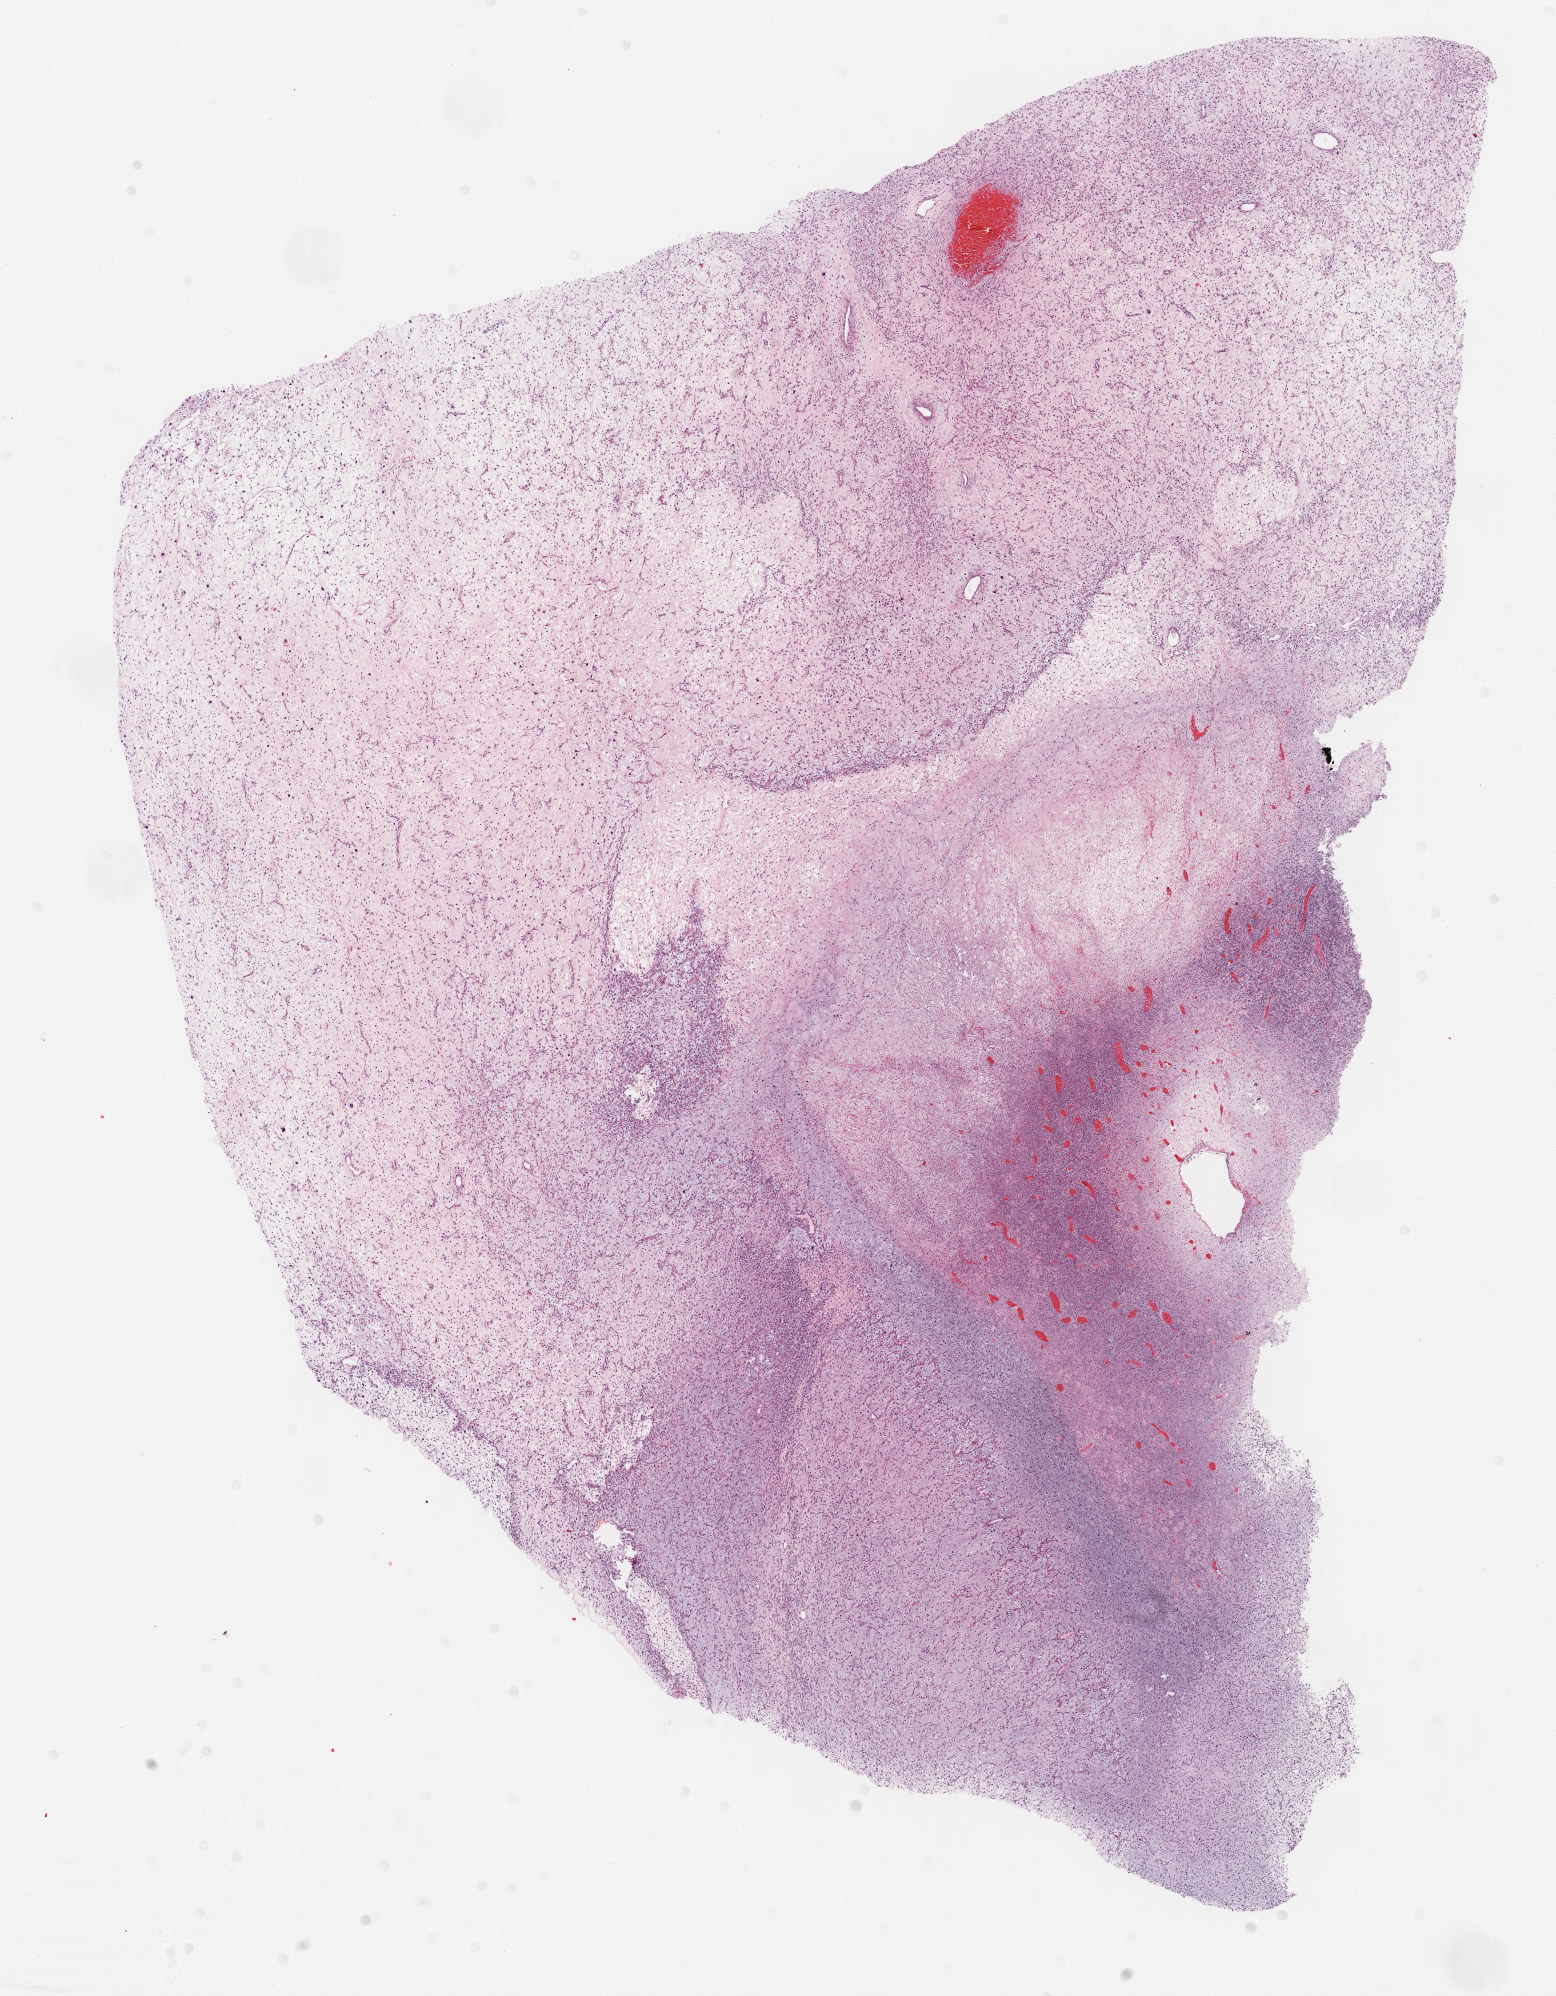
Digitized H&E-stained tissue section (whole slide) — shown as a low-resolution overview of the whole scanned area (about 12.6 x 16.1 mm), FFPE section, sample: primary tumour, retroperitoneum and peritoneum. Male patient; age at initial diagnosis 57 years.
* pathologic diagnosis: Fibromyxosarcoma (retroperitoneum)